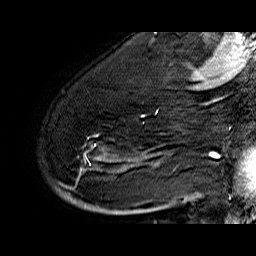
Breast MRI (dynamic contrast-enhanced), one sagittal slice. Position 44 of 60 along the scan axis. Dynamic contrast-enhanced series, time point 2 of 6 at this slice position (early post-contrast). 1.5 T. TE 6.4 ms, TR 32.9 ms. 4 mm slice thickness. 256 × 256 image matrix. Female patient. Case-level facts recorded for this patient, not image findings: setting: breast cancer imaged before/during neoadjuvant chemotherapy; receptor status: HR-positive, HER2-negative.
Annotated regions visible in this slice (semi-automatic segmentation, software-assisted and operator-edited):
- analysis volume of interest (the breast-tissue region the enhancement analysis was run in; not a lesion): bounding box <53,74,176,210> (left, top, right, bottom; pixels)
- tumour enhancement mask (voxels above the 100 % enhancement threshold inside the analysis volume of interest): <57,110,161,207>